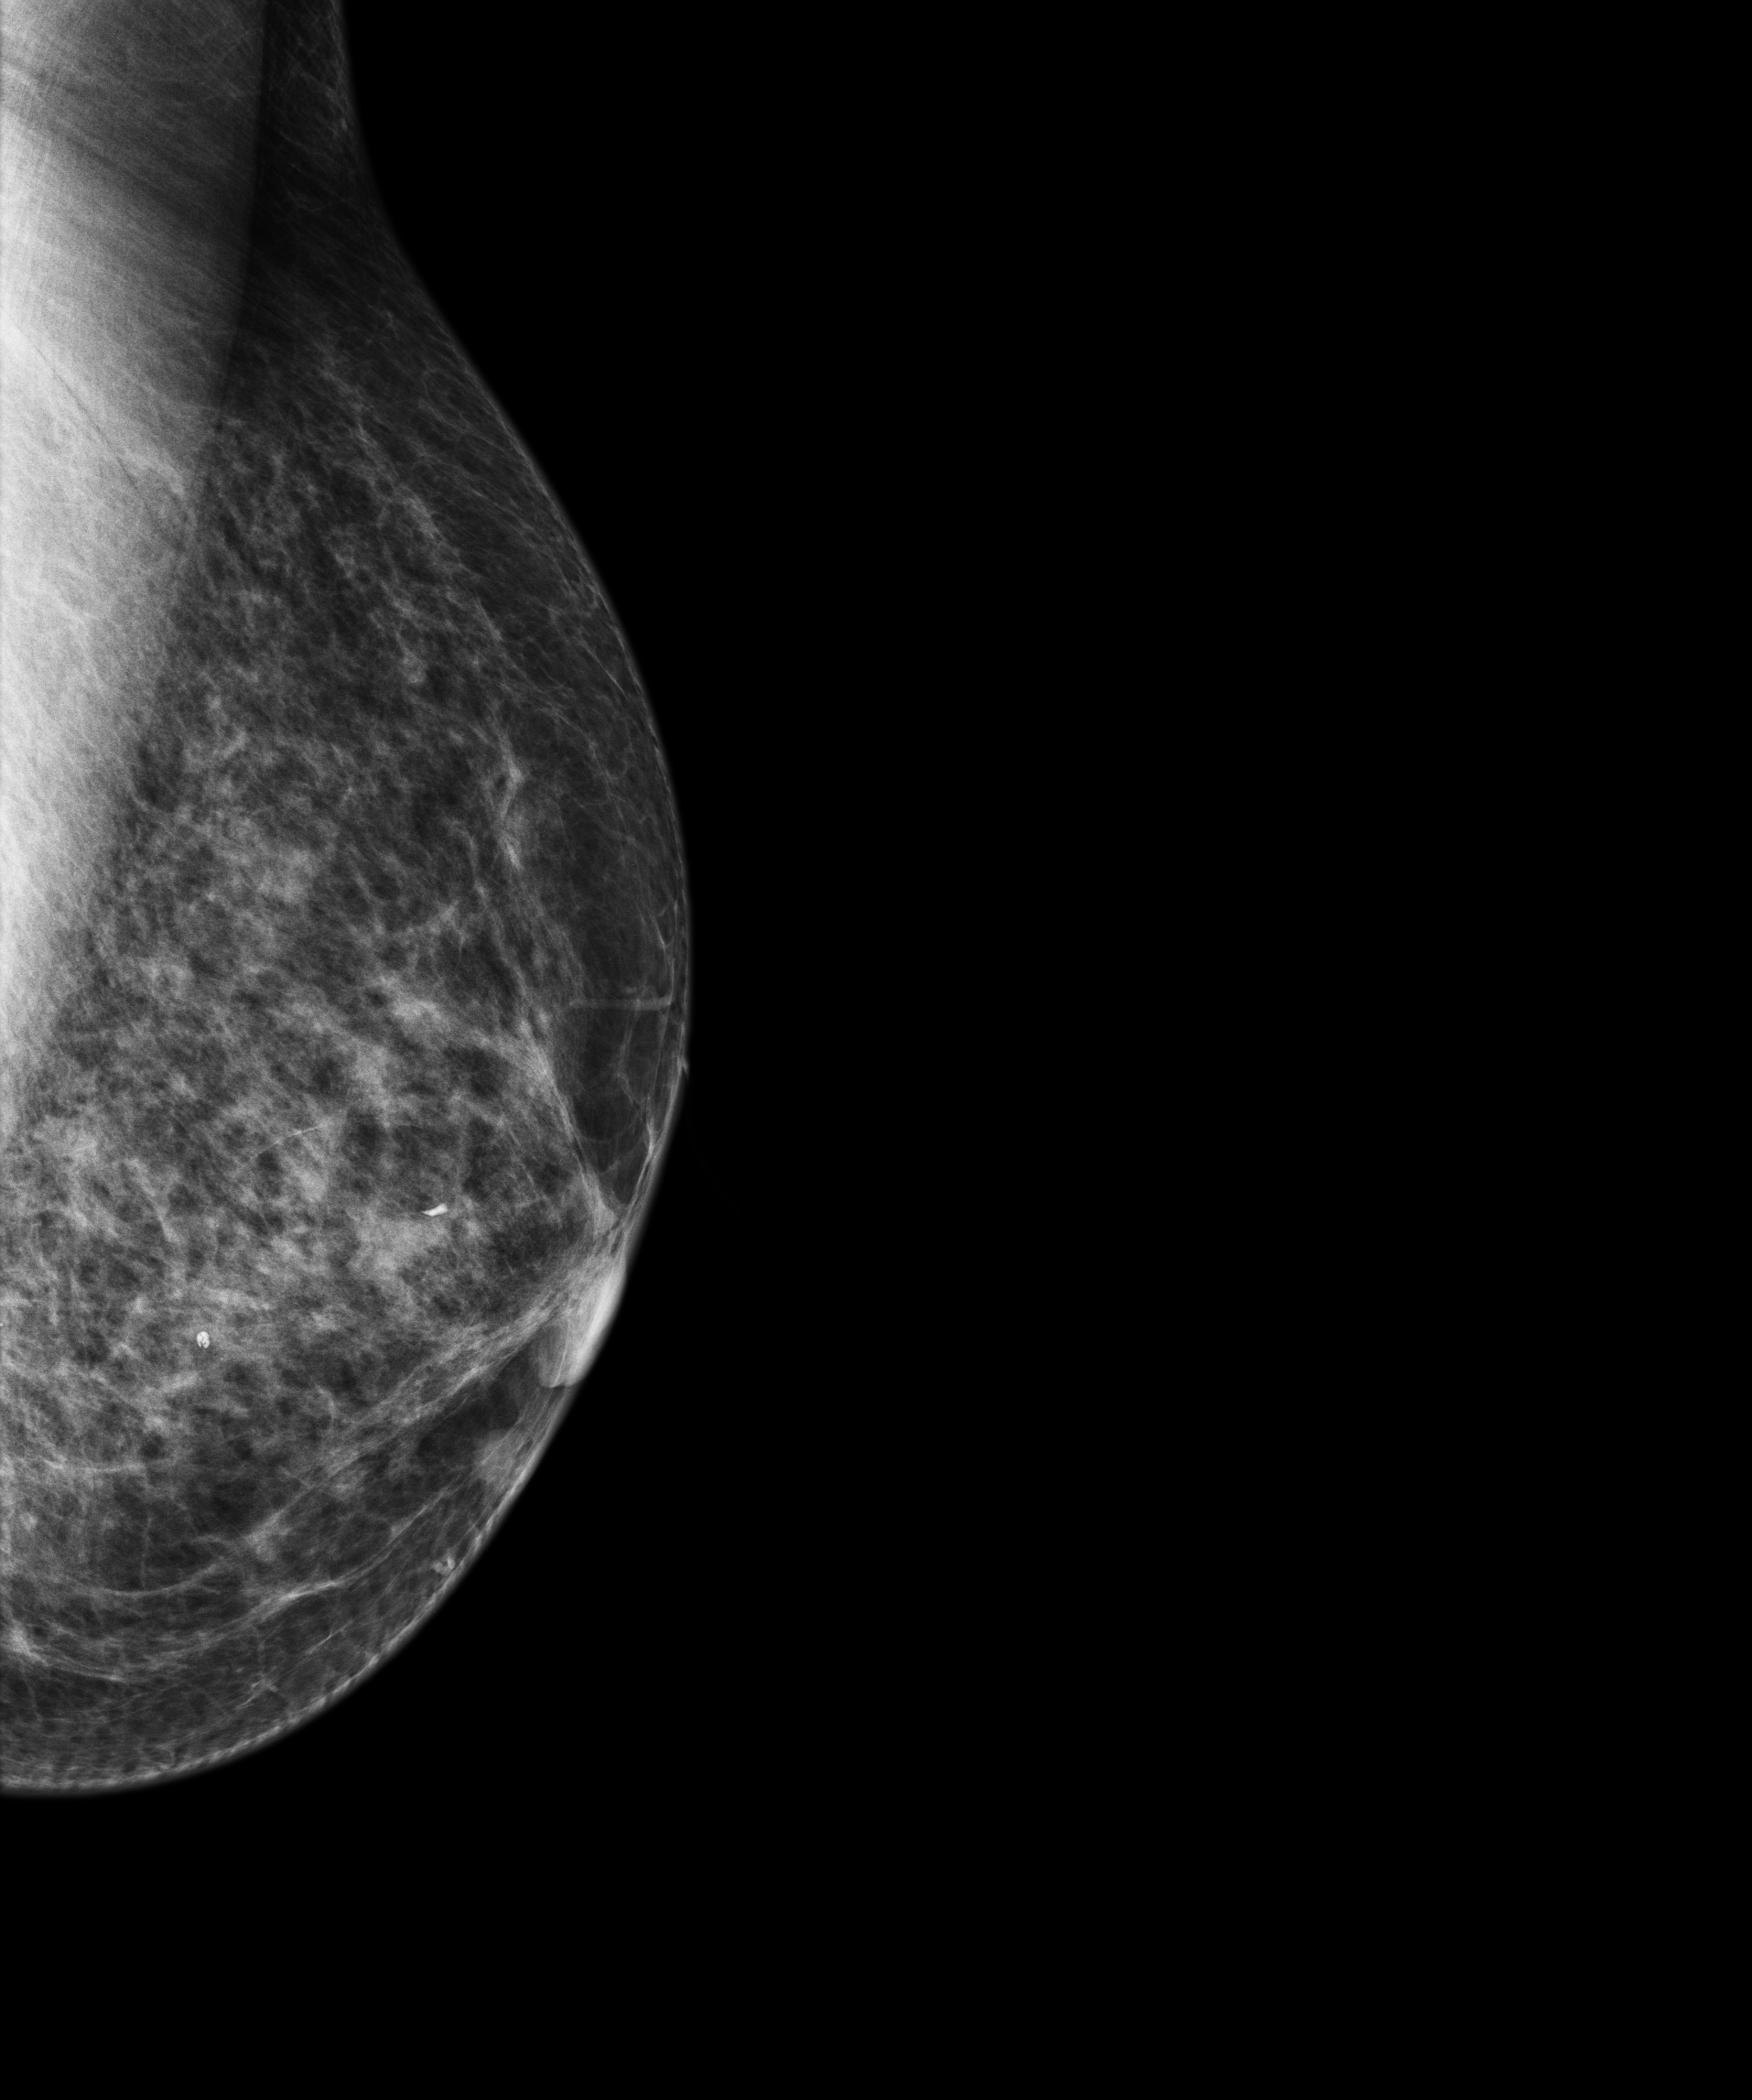
Digital mammogram (FFDM), left breast, laterally exaggerated craniocaudal (XCCL) view, annual screening mammography examination, system: Senographe Essential ADS_56.21.3. Female patient, age 69 years.
- BI-RADS breast density category at the screening exam (both breasts, scale 1–4): 3
- final BI-RADS category for the screening round (tomosynthesis exam, both breasts): category 1
- recall: no recall after this screen